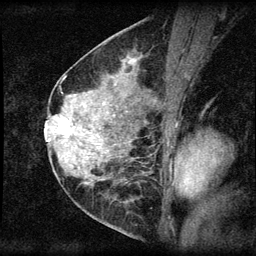
Breast MRI (dynamic contrast-enhanced), one sagittal slice; slice 27 of 60 in the series (ordered by position); dynamic contrast-enhanced series, image 2 of 3 at this slice position (ordered by acquisition); 1.5 T; TE 4.2 ms, TR 8.2 ms; 256 × 256 image matrix. Patient: female, 45 years.
Structures marked on this image (semi-automatically segmented with operator editing):
- analysis volume of interest (the breast-tissue region the enhancement analysis was run in; not a lesion): bounding box (x1, y1, x2, y2) in pixels: (55, 110, 94, 148)
- tumour enhancement mask (voxels above the 70 % enhancement threshold inside the analysis volume of interest): (60, 118, 71, 135)